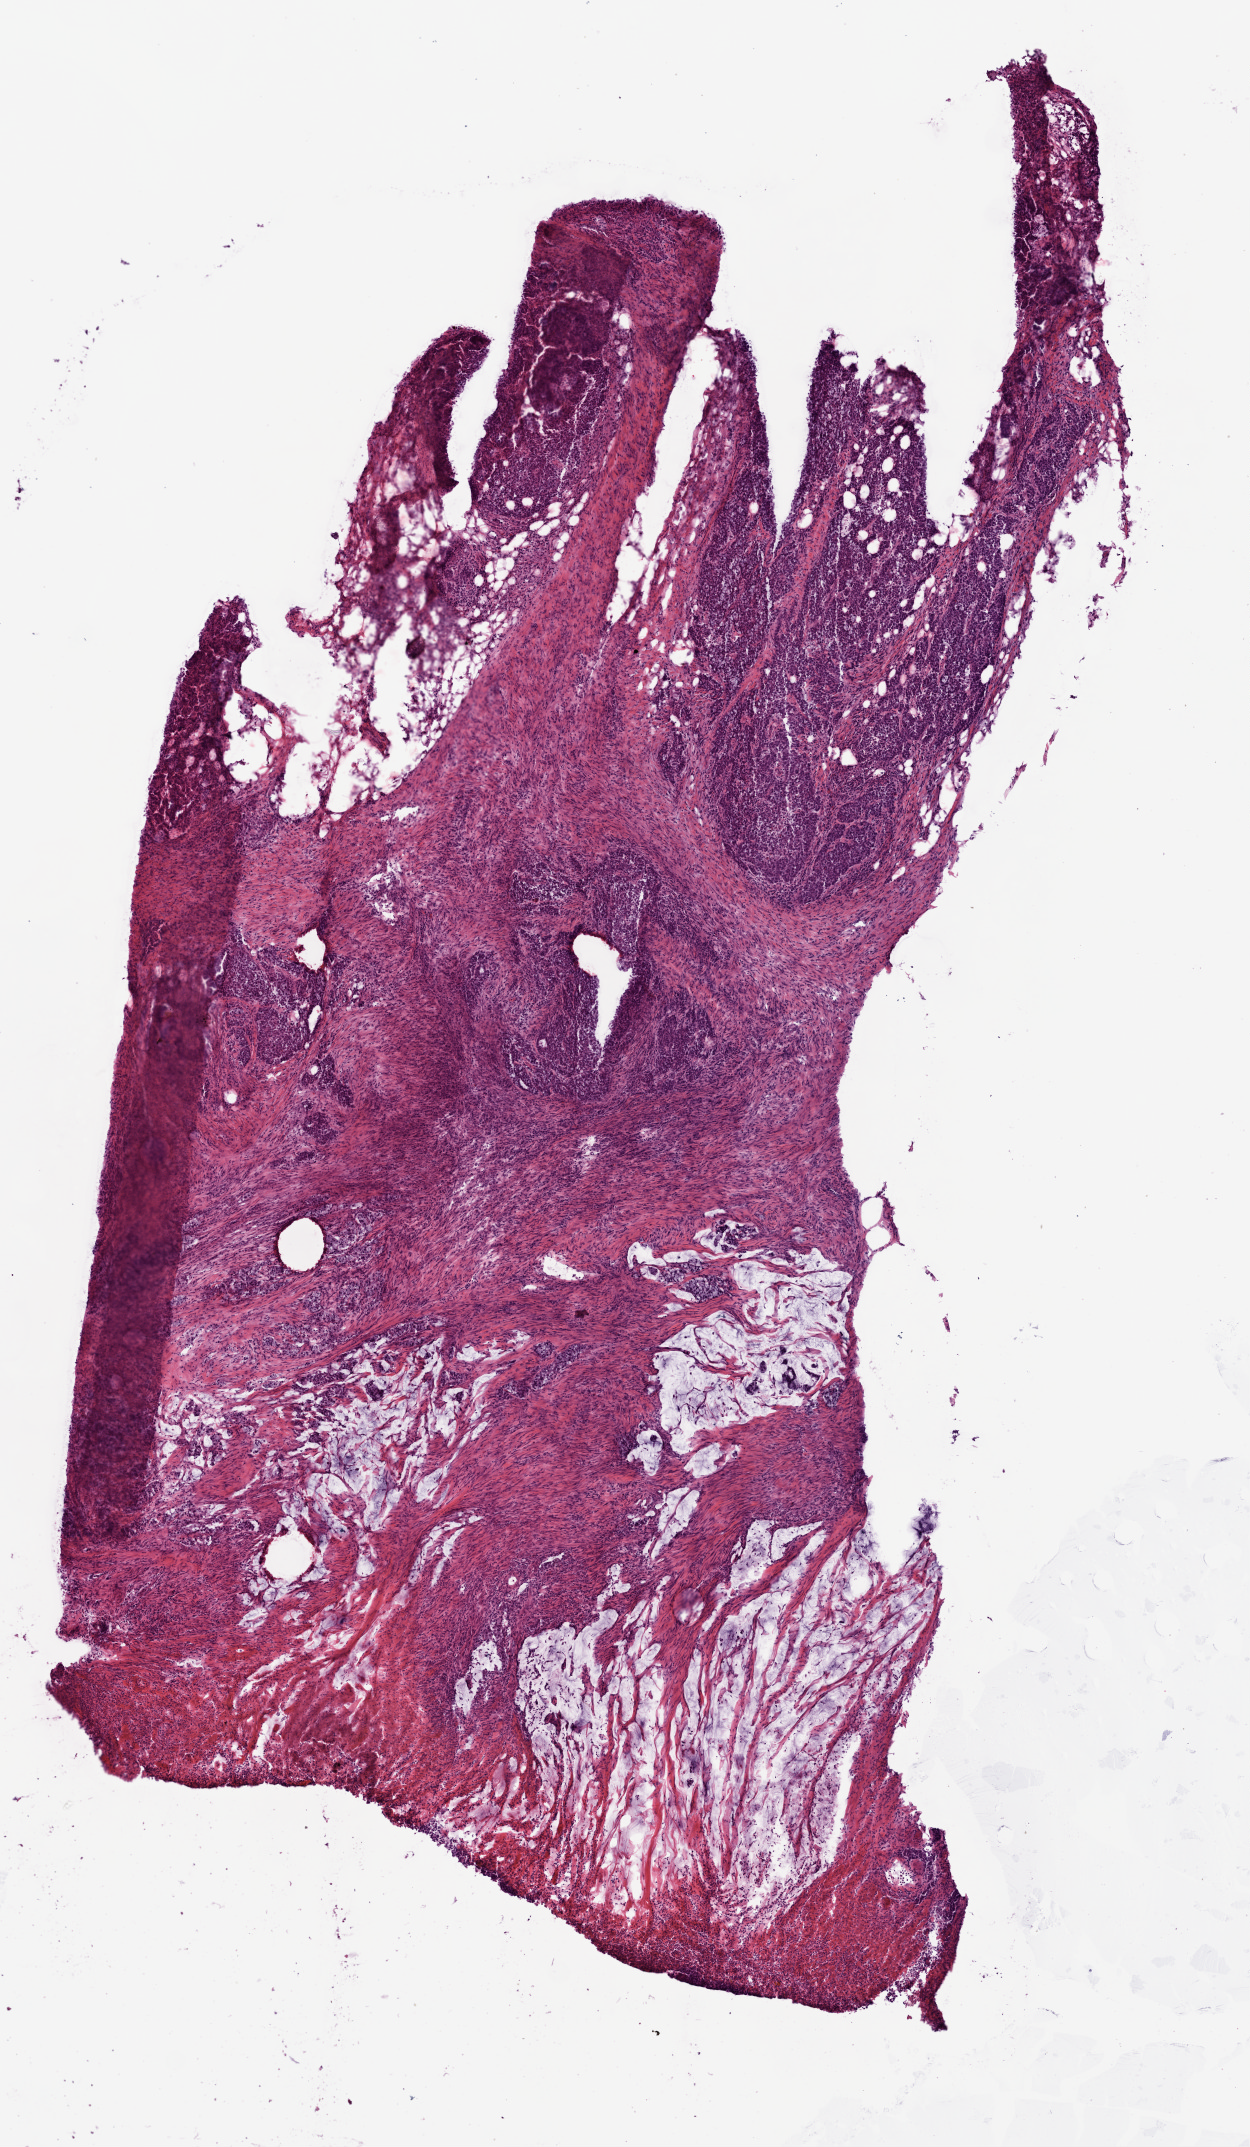
H&E whole-slide image, shown as a low-resolution overview of the whole scanned area (about 5.0 x 8.6 mm). Frozen section. Colon, primary tumour sample. Male patient; age at initial diagnosis 58 years. Composition of this section per pathologist review: tumour cells 50%, tumour nuclei 60%, normal cells 0%, stromal cells 50%, necrosis 0%. Infiltration values recorded for this section: lymphocyte infiltration 30%.
Pathologic diagnosis: Adenocarcinoma, NOS (ascending colon).